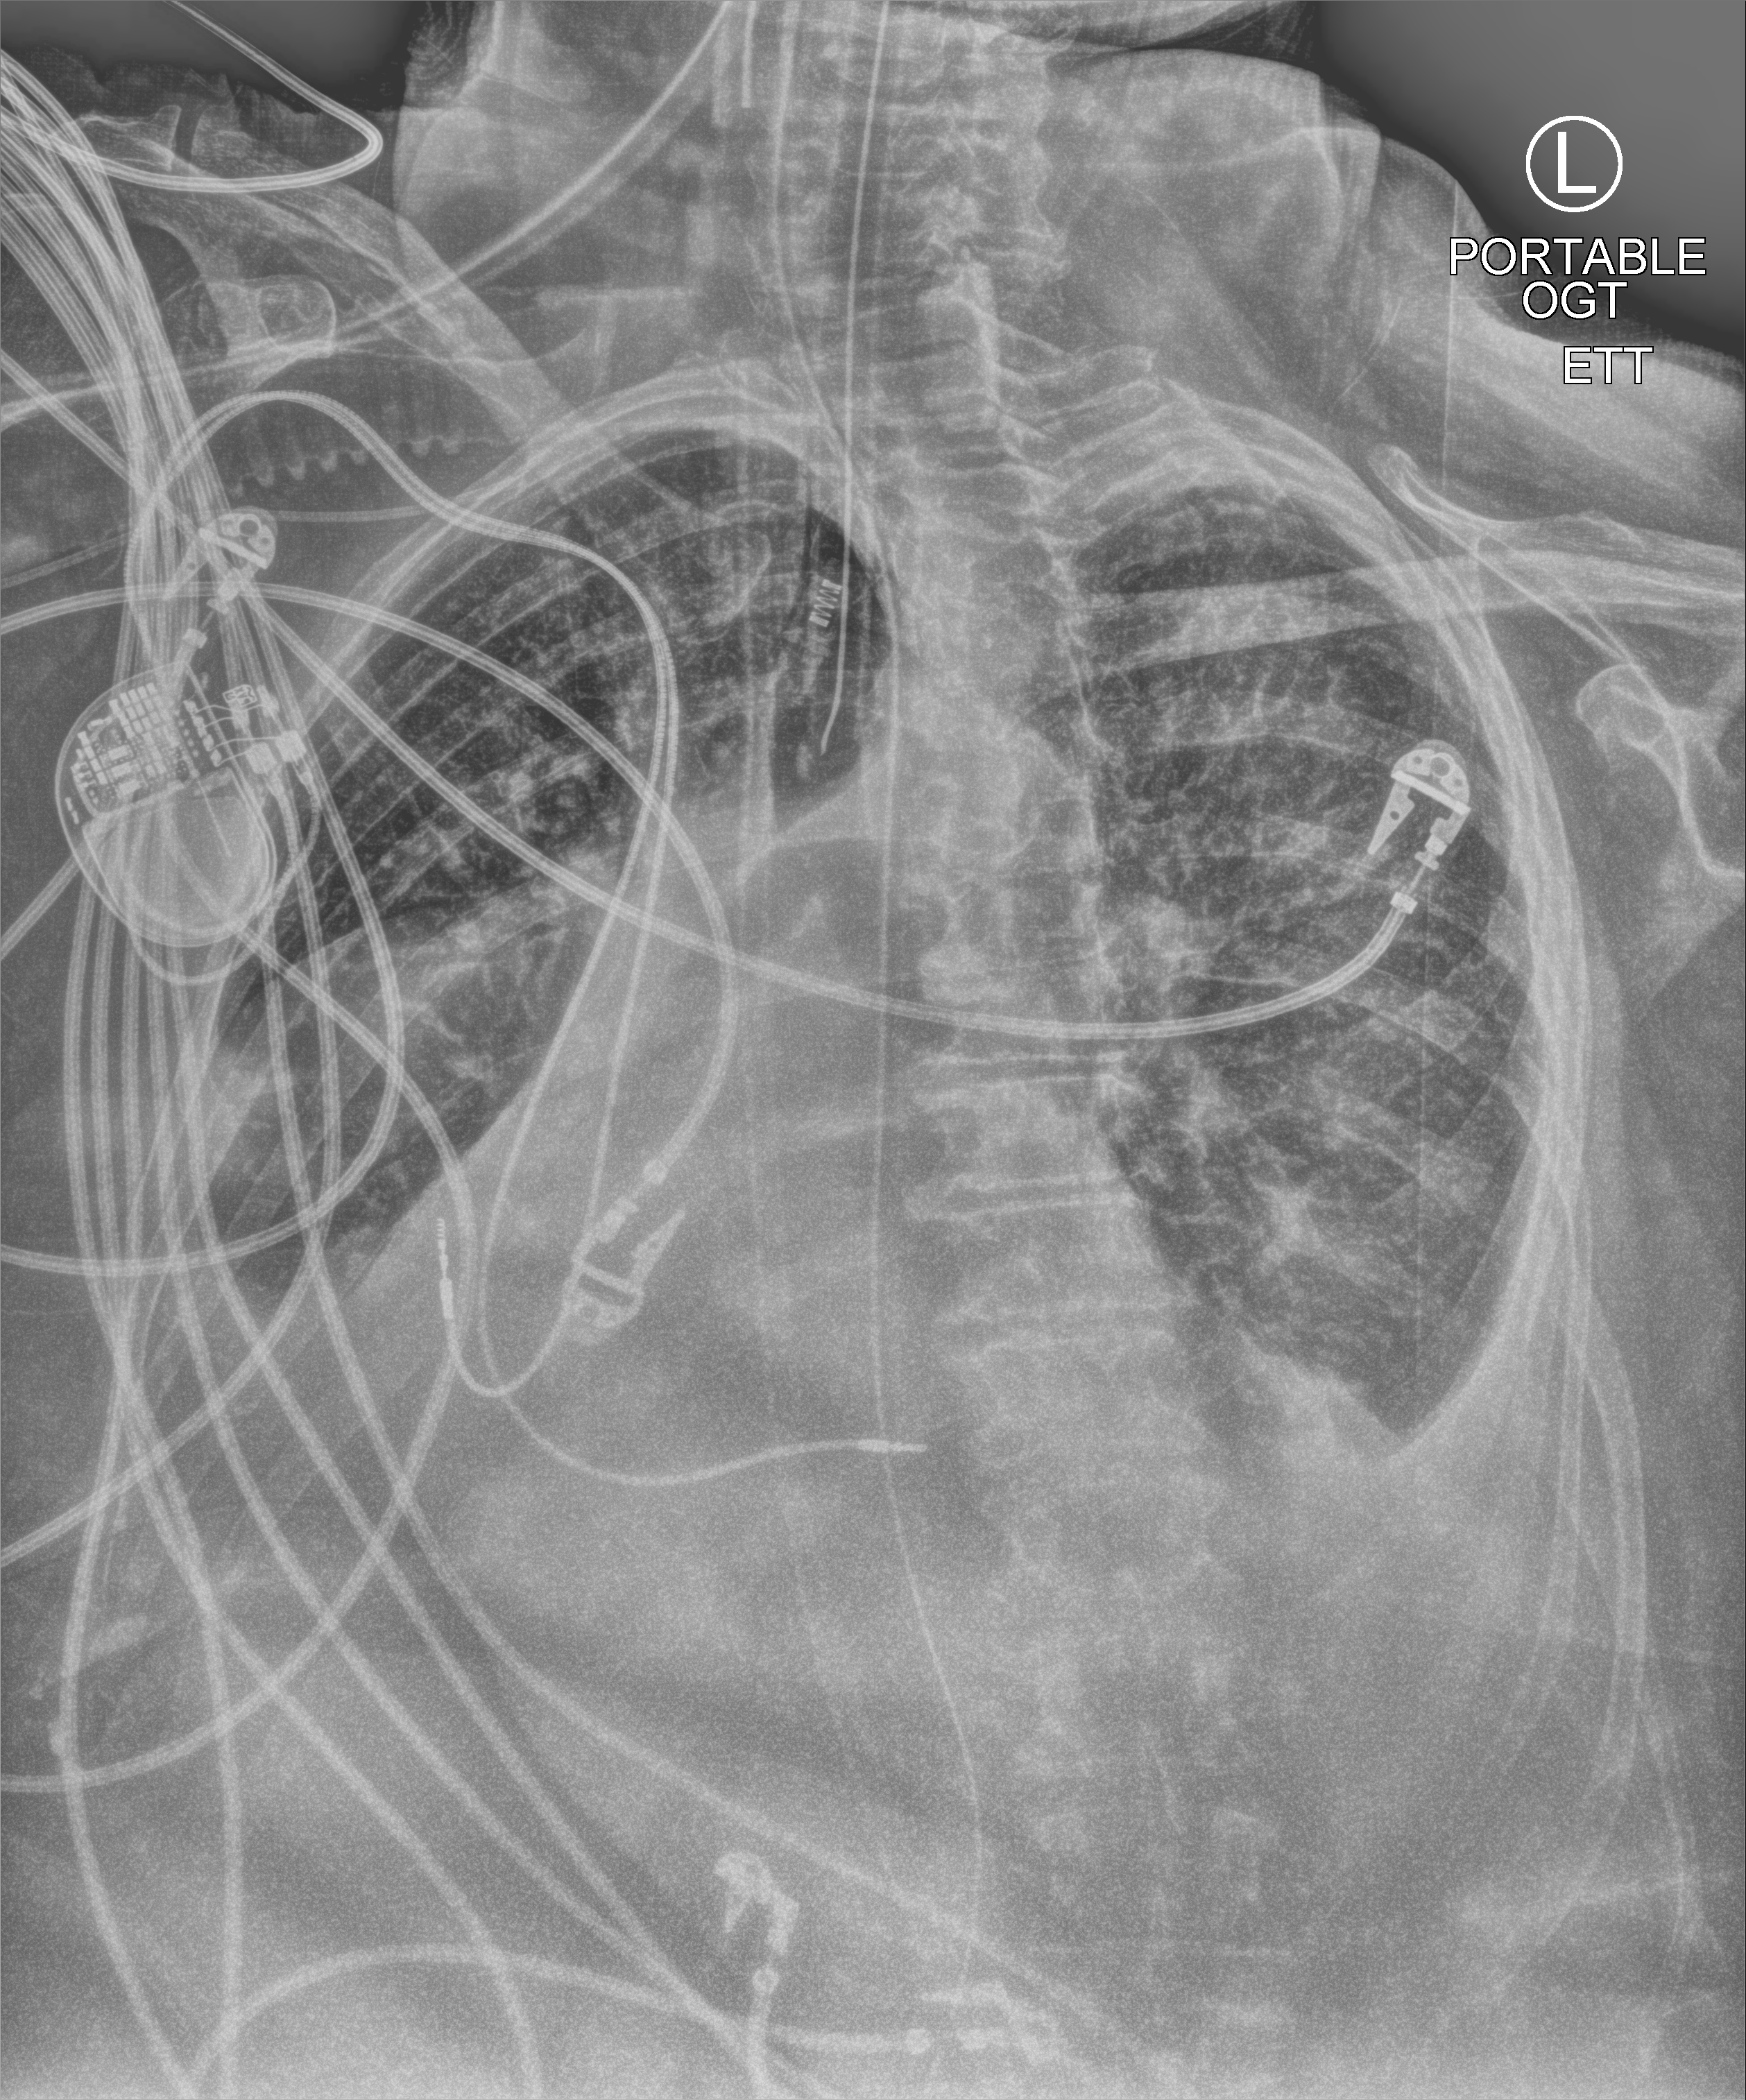
Portable chest radiograph, anteroposterior (AP) projection. Patient hospitalised with COVID-19; female, aged 75–90 years.
Hospital-stay facts (about this admission, not read from this image; timing relative to this image not recorded): admitted to intensive care during this hospital stay: yes.